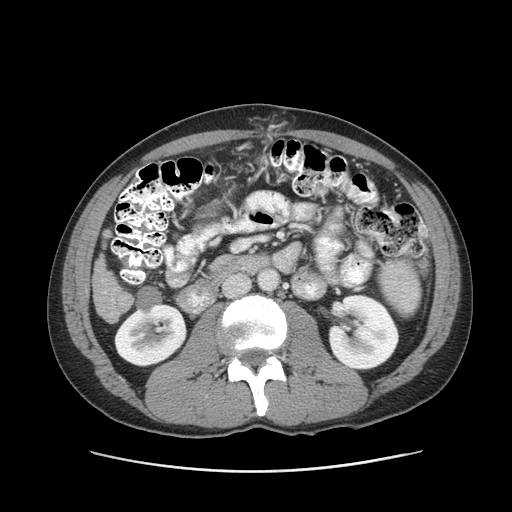
Contrast-enhanced abdominal CT (liver protocol), one axial slice. Slice 28 of 93 in the series (ordered by position). Reconstruction kernel STANDARD. 120 kVp. Soft-tissue window (W 400 / L 40 HU). 512 × 512 image matrix, field of view 380 × 380 mm. From the clinical record (not read from this slice): diagnosis: hepatocellular carcinoma (patient treated with transarterial chemoembolisation; whether this scan precedes or follows treatment is not stated here); TNM stage (as recorded): Stage-II.
Structures marked on this image (semi-automatic segmentation, software-assisted and operator-edited):
- liver parenchyma outside the tumour (the mass and vessels are separate outlines, so this box may not span the whole liver): bounding box (x1, y1, x2, y2) in pixels: (92, 255, 132, 322)